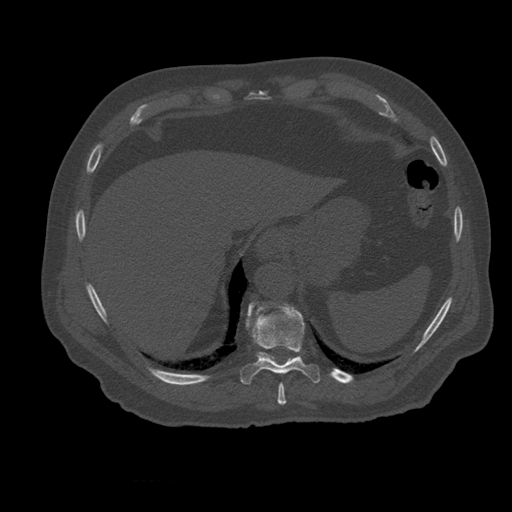
CT including the spine, one axial slice; slice 301 of 399 in the series (ordered by position); 120 kVp; bone window (W 1800 / L 400 HU); 1.25 mm slice thickness; 512 × 512 image matrix, field of view 407 × 407 mm. Patient age 73 years. Case-level facts recorded for this patient, not image findings: primary cancer: prostate; vertebrae with lytic lesions (as recorded): L2.
Outlined on this slice (semi-automatic segmentation, software-assisted and operator-edited):
- T10 vertebra: box from (x=241, y=304) to (x=320, y=385) px
- T11 vertebra: (x=256, y=304)–(x=276, y=362)
- T9 vertebra: (x=278, y=384)–(x=287, y=405)